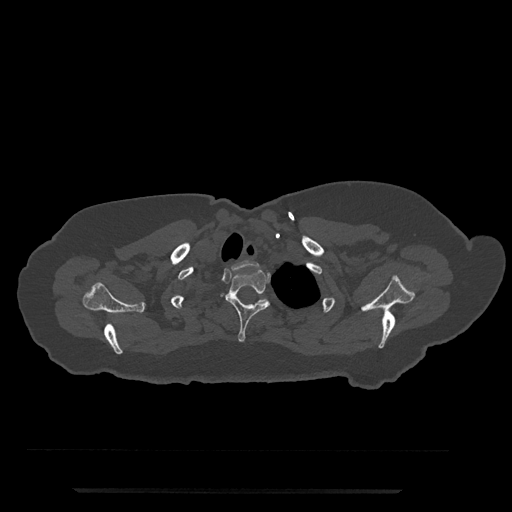
CT including the spine, one axial slice; slice 671 of 797 in the series (ordered by position); bone window (W 1800 / L 400 HU); 512 × 512 image matrix, field of view 440 × 440 mm. Patient: female, 51 years. Case-level facts recorded for this patient, not image findings: primary cancer: neuro; vertebrae with lytic lesions (as recorded): T8.
Structures marked on this image (semi-automatic segmentation, software-assisted and operator-edited):
- T1 vertebra: bounding box <232,260,258,270> (left, top, right, bottom; pixels)
- T2 vertebra: <226,268,270,342>
- T3 vertebra: <235,295,268,303>